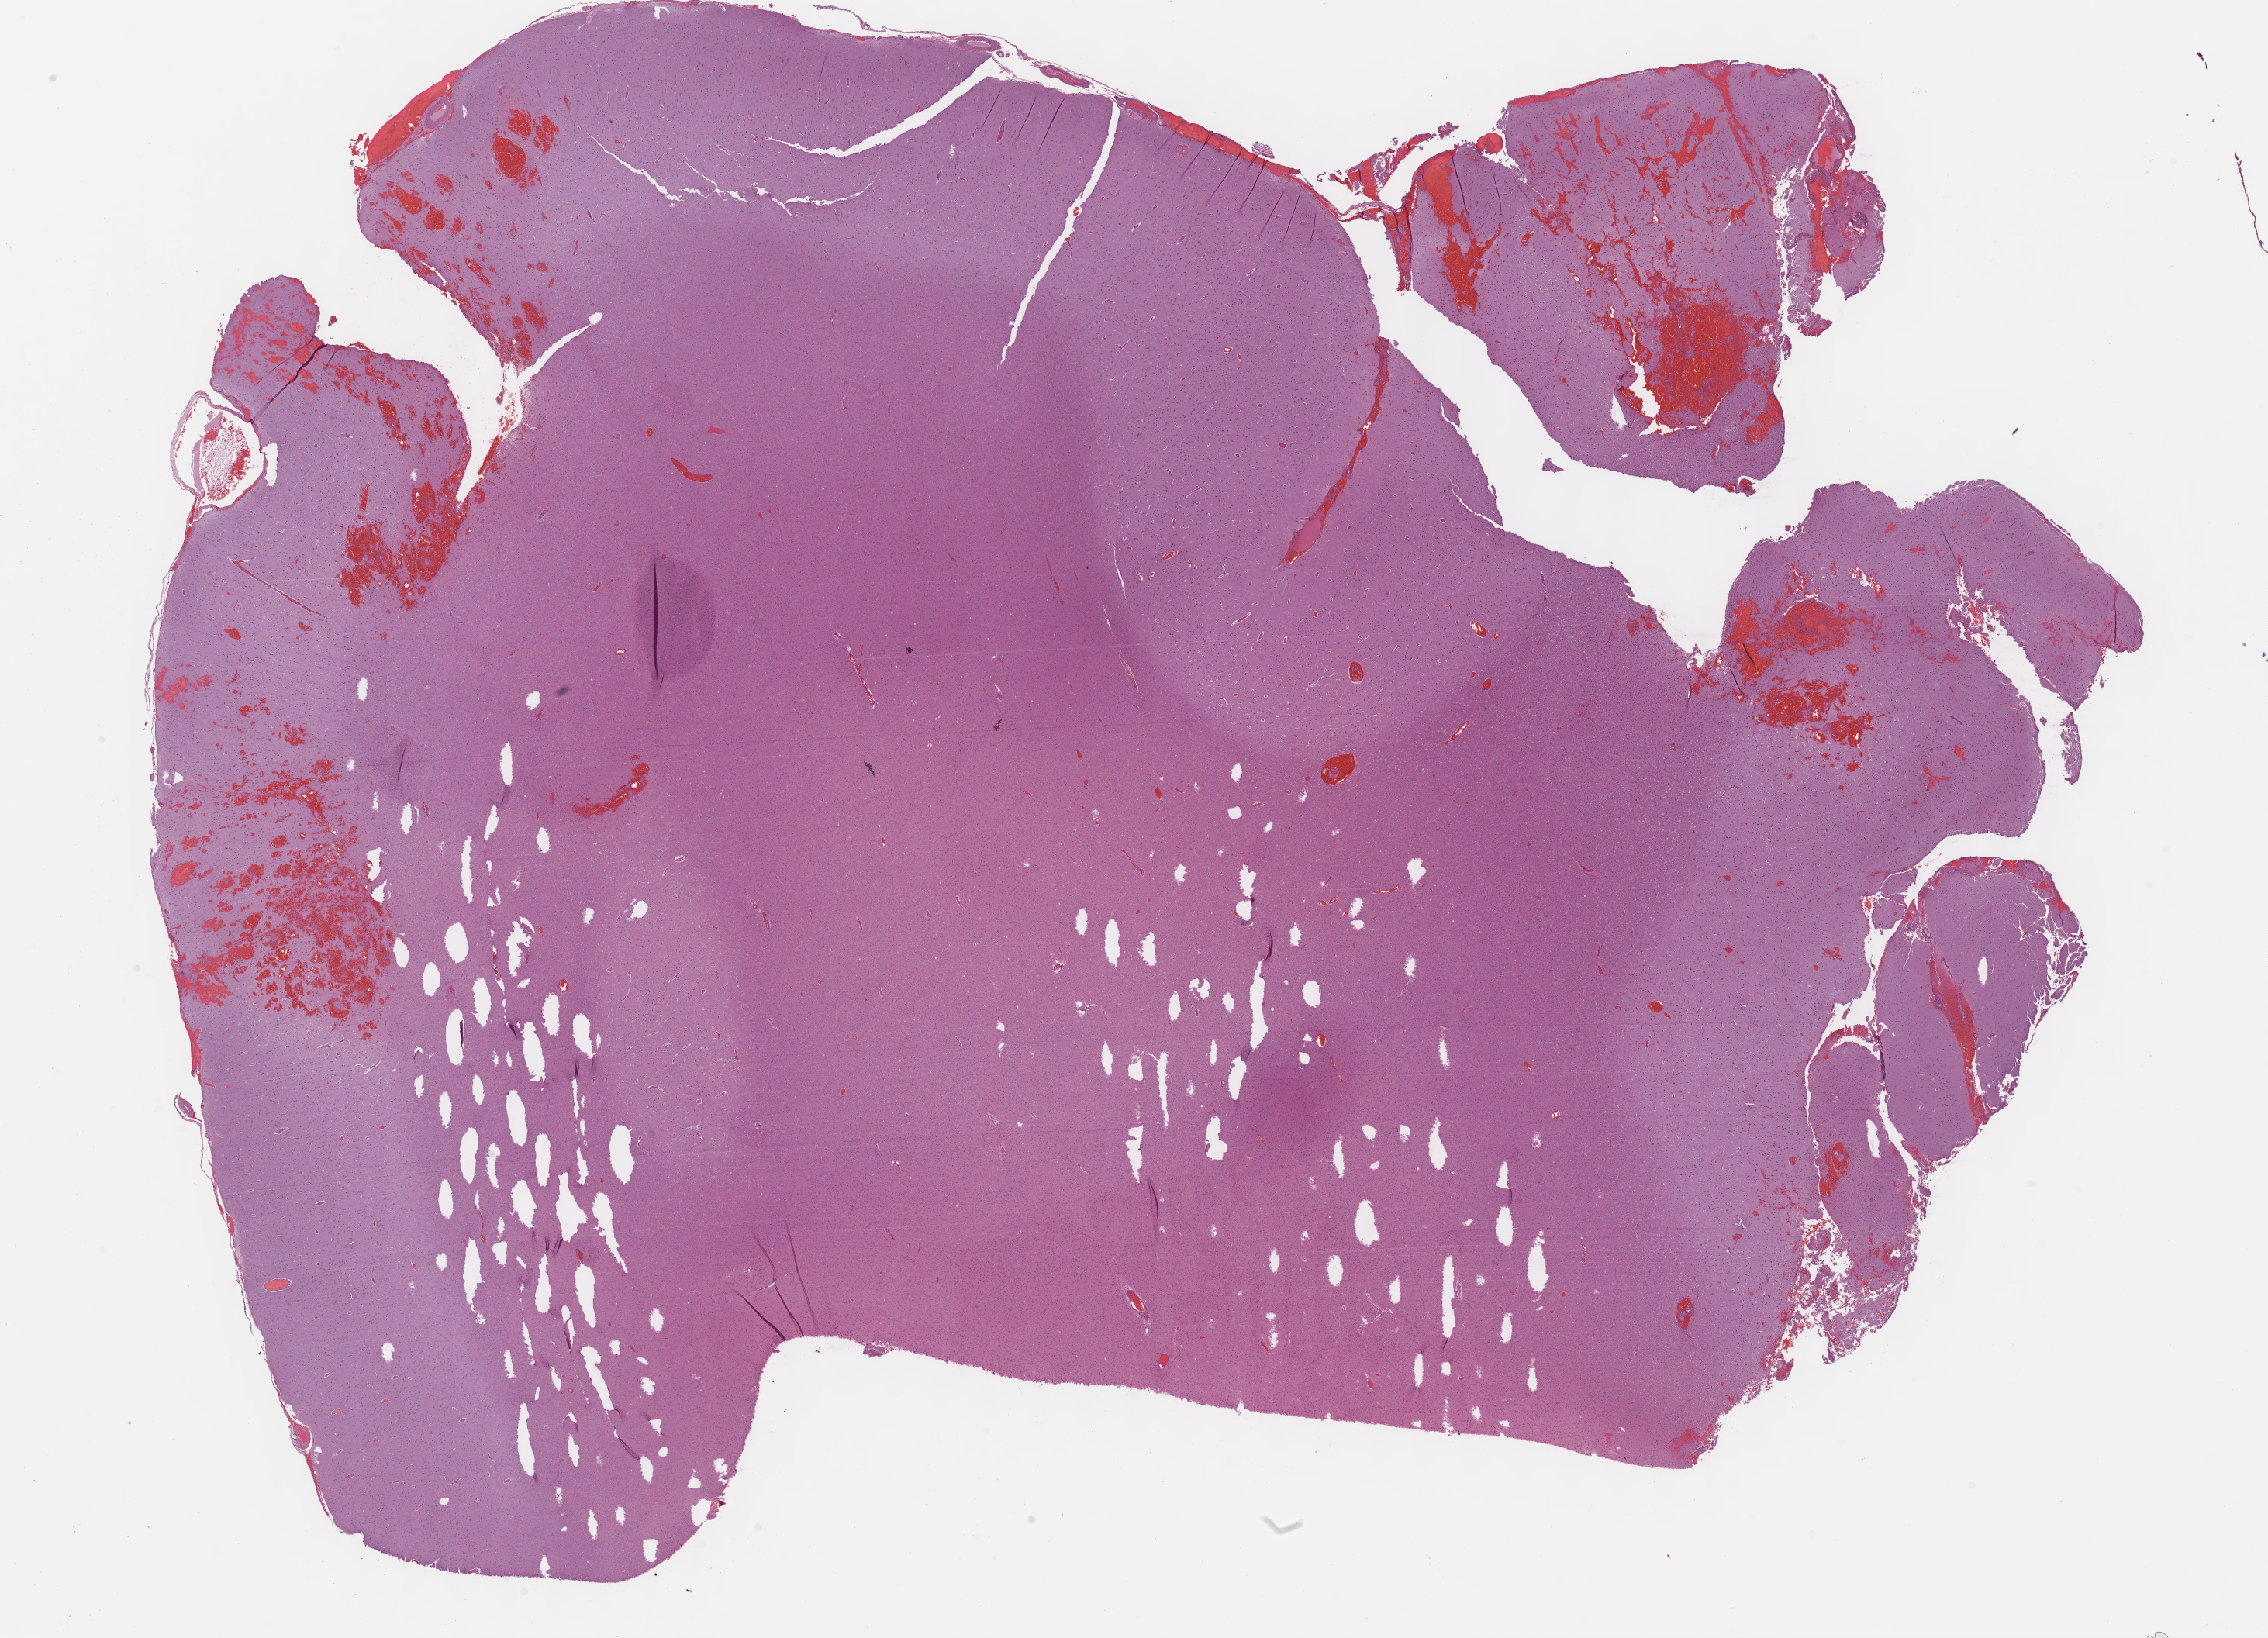
Whole-slide histology image, H&E — whole scanned area (about 23.7 x 17.1 mm) shown as a low-resolution overview; FFPE section; primary tumour sample from the brain. Male patient; age at initial diagnosis 61 years. Histologic grade: G2 (moderately differentiated).
Diagnosis: Mixed glioma (cerebrum).